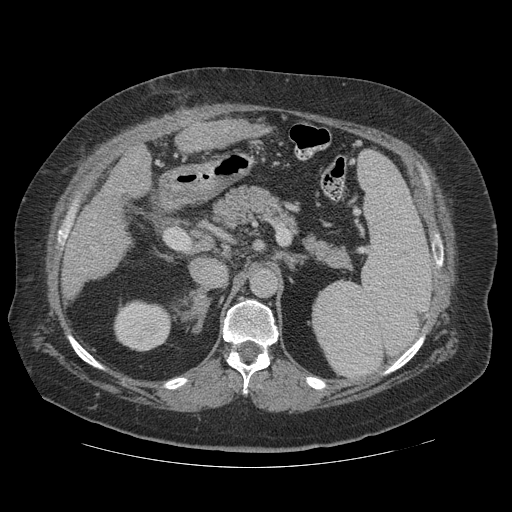
Contrast-enhanced abdominal CT (liver protocol), one axial slice. Slice 64 of 121 in the series (ordered by position). Reconstruction kernel STANDARD. 140 kVp. Soft-tissue window (W 400 / L 40 HU). 2.5 mm slice thickness. 512 × 512 image matrix, field of view 420 × 420 mm. From the clinical record (not read from this slice): diagnosis: hepatocellular carcinoma (patient treated with transarterial chemoembolisation; whether this scan precedes or follows treatment is not stated here); TNM stage (as recorded): Stage-IIIA; Child-Pugh class: A; tumour size: 7.4 cm.
Structures marked on this image (semi-automatic segmentation, software-assisted and operator-edited):
- liver parenchyma outside the tumour (the mass and vessels are separate outlines, so this box may not span the whole liver): bounding box [x1, y1, x2, y2] px = [88, 120, 258, 232]